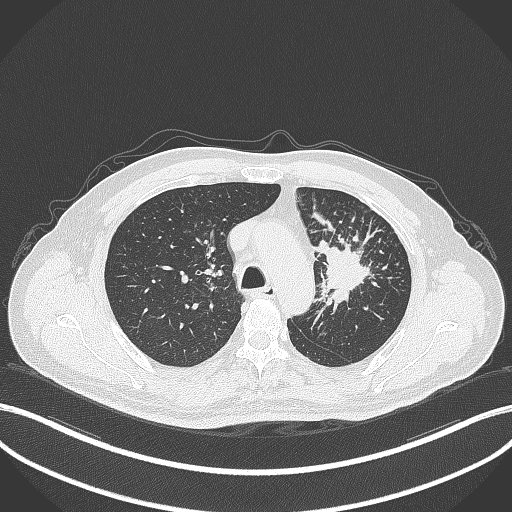
Chest CT, one axial slice. Position 258 of 386 along the scan axis. Reconstruction kernel B70f. 120 kVp. Lung window (W 1500 / L -600 HU). 512 × 512 image matrix. Patient: male, 69 years. Case-level facts recorded for this patient, not image findings: clinical TNM (as recorded): T2a N2 M0; histopathological grade: G2-3.
Annotated regions visible in this slice (bounding box drawn by a radiologist):
- lung tumour (recorded histology: adenocarcinoma): bounding box (x1, y1, x2, y2) in pixels: (313, 232, 373, 311)